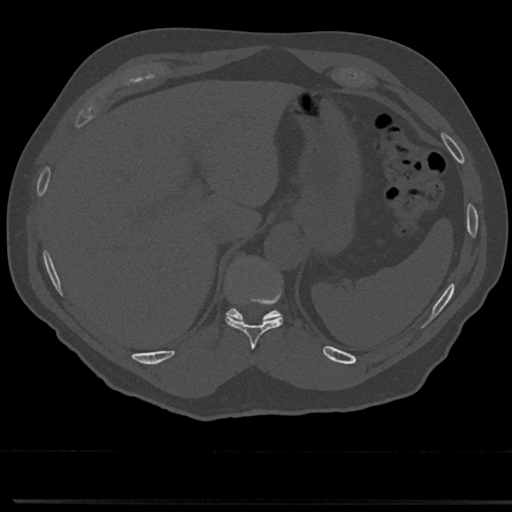
CT including the spine, one axial slice; slice 240 of 817 in the series (ordered by position); reconstruction kernel Br40s/3; bone window (W 1800 / L 400 HU); 512 × 512 image matrix, field of view 355 × 355 mm. Male patient, age 61 years. Case-level facts recorded for this patient, not image findings: primary cancer: prostate.
Outlined on this slice (semi-automatically segmented with operator editing):
- T10 vertebra: box from (x=226, y=258) to (x=283, y=347) px
- T11 vertebra: (x=228, y=311)–(x=279, y=321)